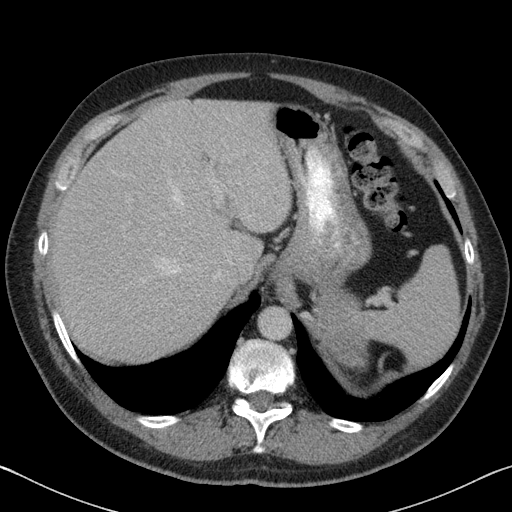
Contrast-enhanced abdominal CT, one axial slice; position 64 of 88 along the scan axis; intravenous contrast given; soft-tissue window (W 400 / L 40 HU); 3 mm slice thickness; 512 × 512 image matrix. Male patient, age 51 years. From the clinical record (not read from this slice): diagnosis: adrenocortical carcinoma; tumour side: left adrenal; tumour size at pathology: 16.5 cm; Ki-67 index: 30 %; stage (as recorded): 2.
Annotated regions visible in this slice (semi-automatically segmented with operator editing):
- mass: box from (x=315, y=291) to (x=364, y=368) px